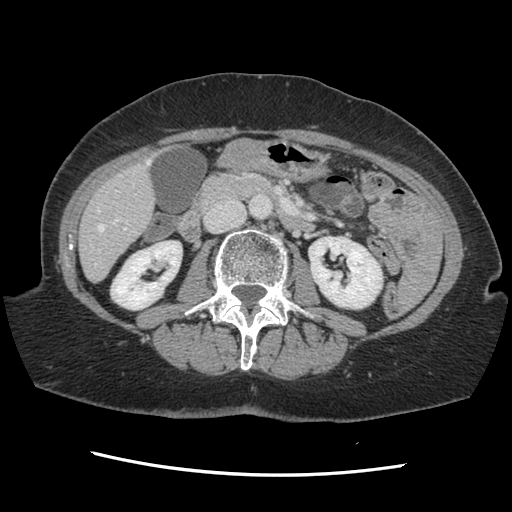
Contrast-enhanced abdominal CT, one axial slice. Position 49 of 141 along the scan axis. 120 kVp. Soft-tissue window (W 400 / L 40 HU). 2.5 mm slice thickness. 512 × 512 image matrix. Female patient, age 61 years. Case-level facts recorded for this patient, not image findings: diagnosis: colorectal cancer liver metastases, imaged before liver resection; multiple liver metastases: no; largest metastasis: 2.4 cm.
Outlined on this slice (manually delineated by an expert):
- hepatic veins: bounding box (x1, y1, x2, y2) in pixels: (95, 160, 150, 266)
- liver: (81, 161, 155, 281)
- planned liver remnant (the part of the liver to remain after resection): (81, 190, 154, 281)
- portal vein (with intrahepatic branches): (98, 228, 126, 251)